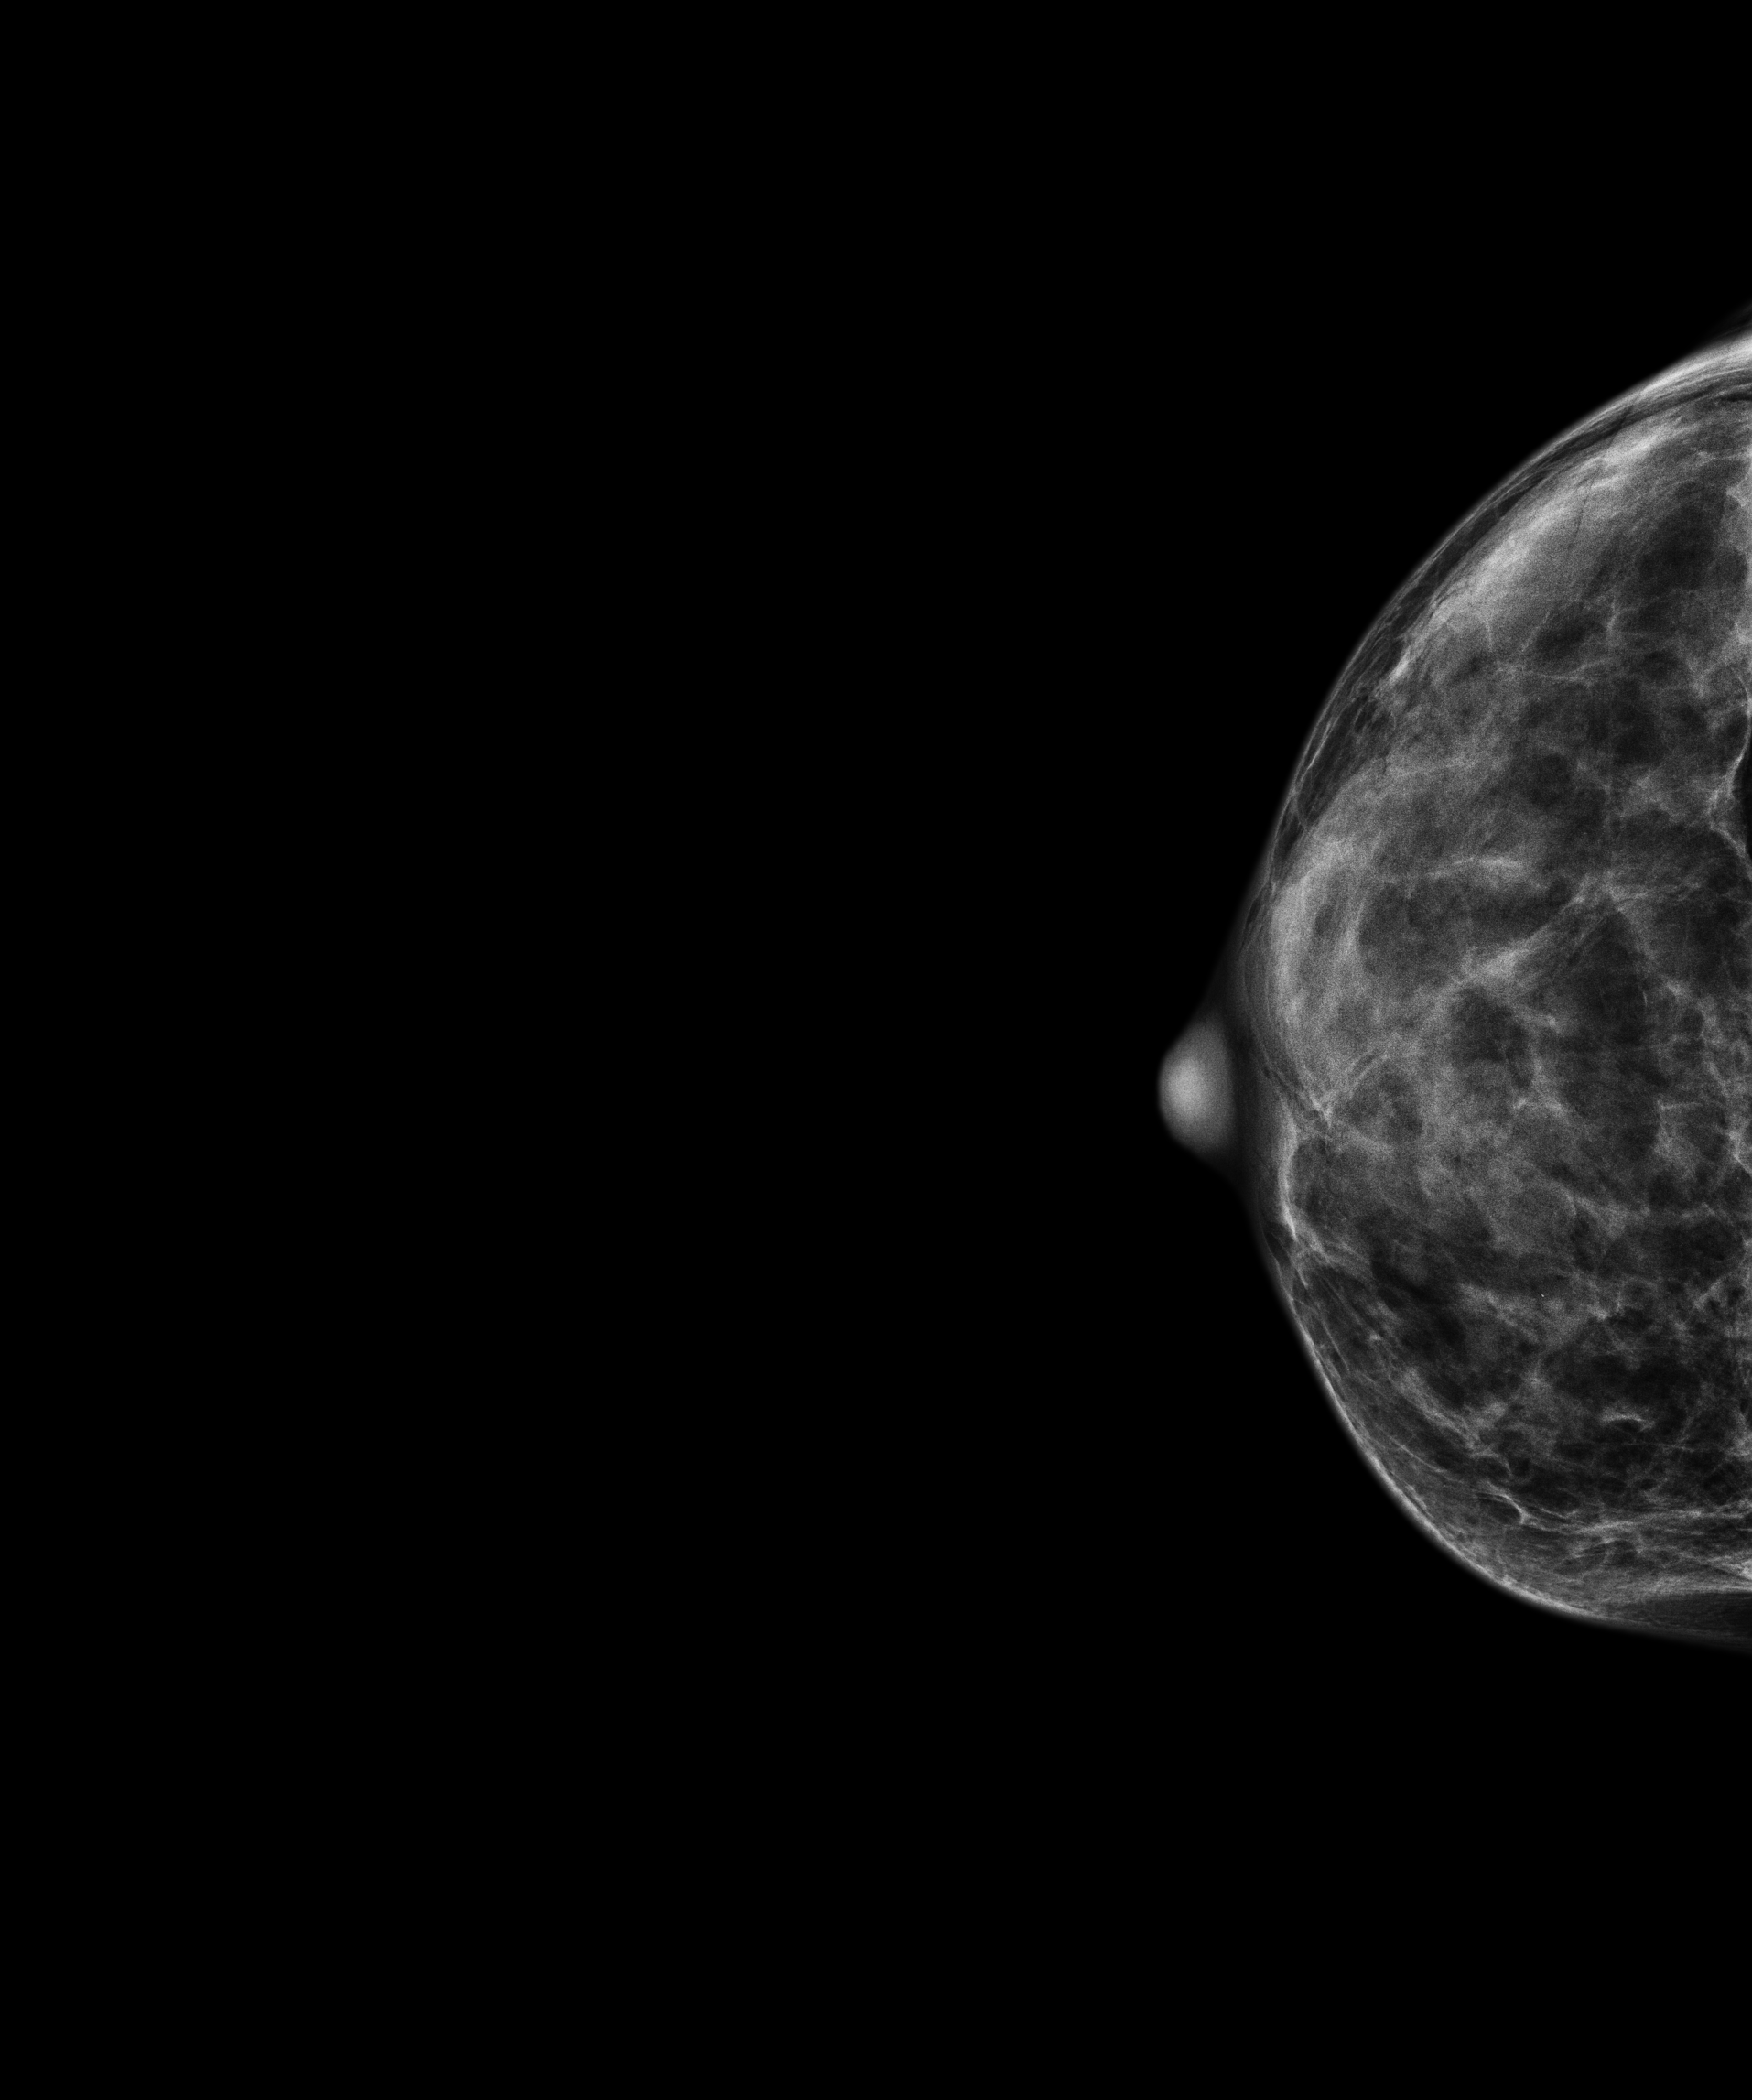
Screening examination, compressed breast thickness 21.4 mm, system: Senographe Pristina. Female patient, age 55 years.
Image type: full-field digital mammogram. Breast: right. Projection: cranio-caudal projection.